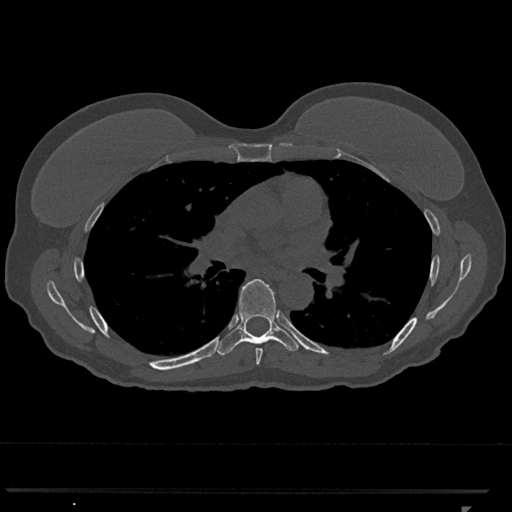
CT including the spine, one axial slice; position 727 of 793 along the scan axis; reconstruction kernel Br40s/3; 120 kVp; bone window (W 1800 / L 400 HU); 512 × 512 image matrix, field of view 380 × 380 mm. Patient: female, 62 years. From the clinical record (not read from this slice): primary cancer: renal.
Outlined on this slice (semi-automatically segmented with operator editing):
- T6 vertebra: bounding box <255,348,263,365> (left, top, right, bottom; pixels)
- T7 vertebra: <215,279,299,356>